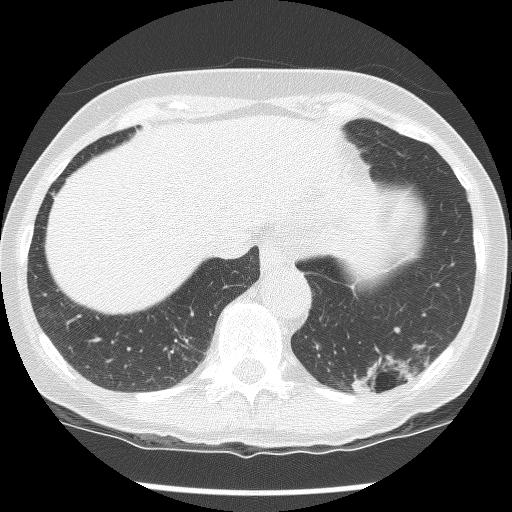
Chest CT (low-dose screening protocol), one axial image; second screening round (one year after baseline); lung window (W 1500 / L -600 HU); 2.5 mm slice thickness; 512 × 512 image matrix. Female participant, aged 61 years at enrolment. Current smoker at enrolment.
- Expert-annotated lung lesion, bounding box (x1, y1, x2, y2) in pixels: (327, 311, 439, 412).
- The screening reader recorded 2 non-calcified nodules or masses ≥4 mm on this exam (left lower lobe, left lower lobe); which of them this box marks is not recorded.
- Official screen result: positive, no significant change: stable abnormalities potentially related to lung cancer, unchanged since the prior screening exam.
- Lung cancer was diagnosed 585 days after this screen: non-small cell carcinoma, left lower lobe, poorly differentiated (G3), stage IB (AJCC 6th edition), 100 mm at pathology.